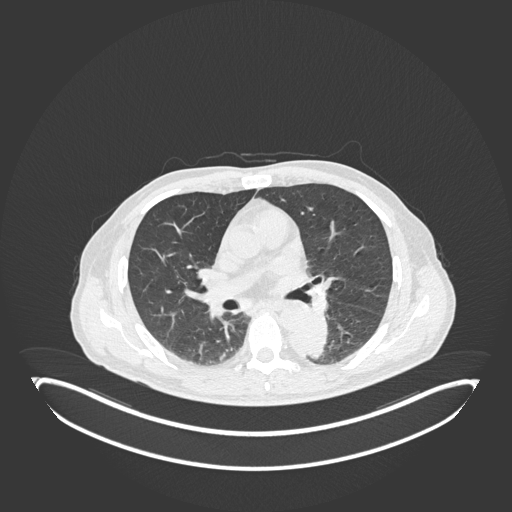
Chest CT, one axial slice; slice 112 of 251 in the series (ordered by position); lung window (W 1500 / L -600 HU); 1 mm slice thickness; 512 × 512 image matrix, field of view 500 × 500 mm. Patient: male, 72 years. From the clinical record (not read from this slice): clinical TNM (as recorded): T2b N0 M1.
Outlined on this slice (rectangle marked by the reading radiologist):
- lung tumour (recorded histology: adenocarcinoma): bounding box (x1, y1, x2, y2) in pixels: (286, 314, 331, 359)